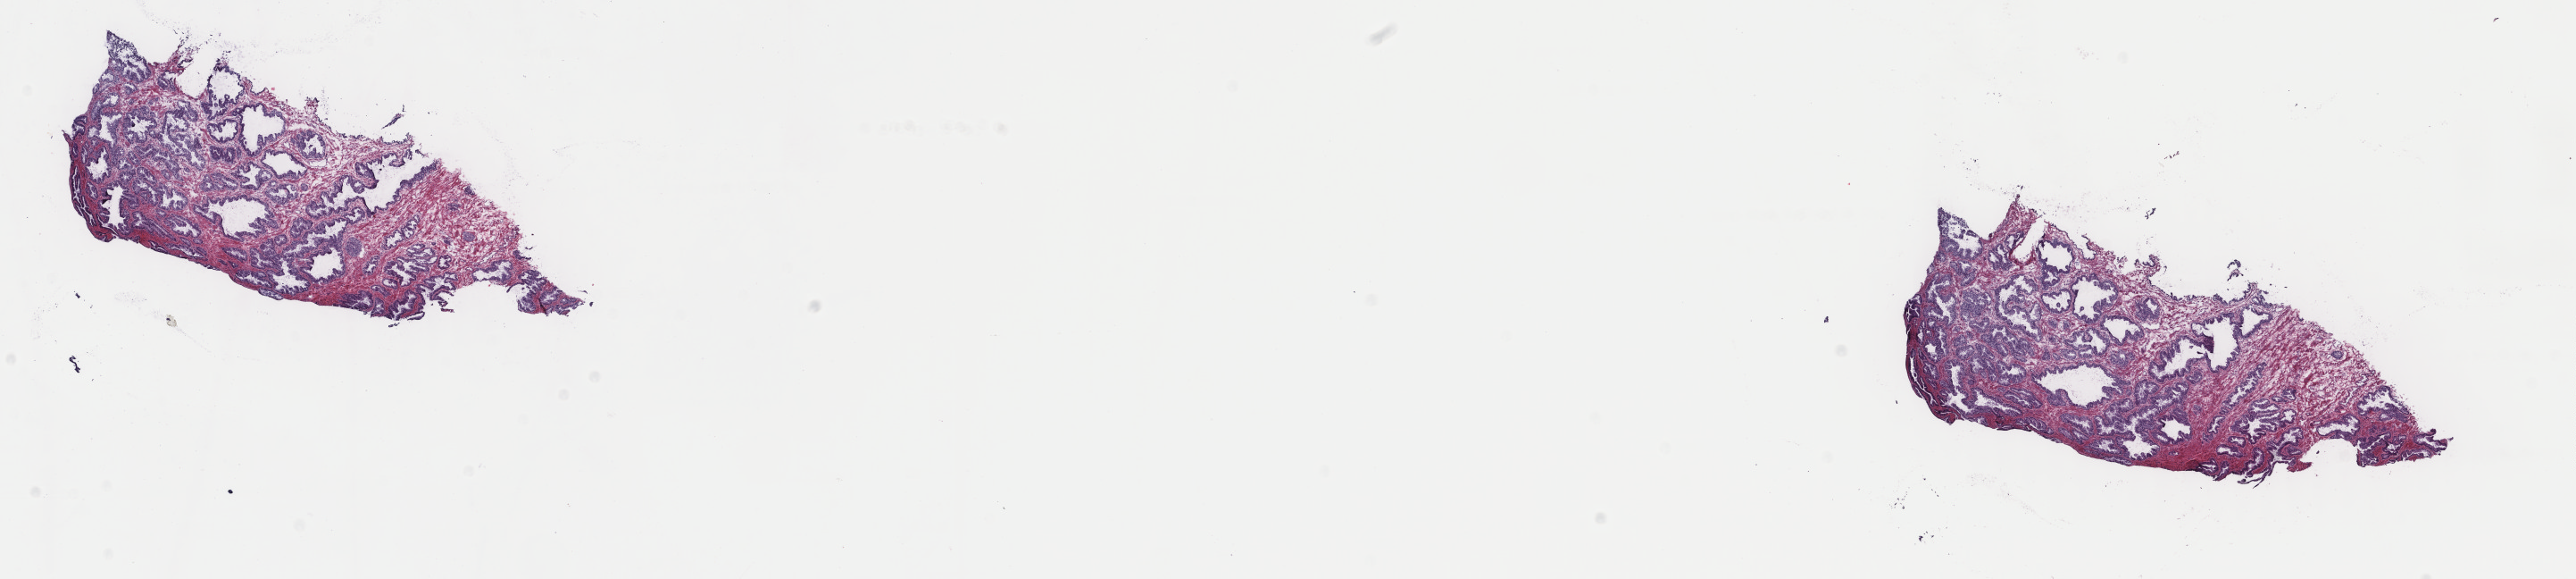
Hematoxylin and eosin (H&E) stained whole-slide image — shown as a low-resolution overview of the whole scanned area (about 22.9 x 5.1 mm); frozen section from the top of the tissue portion; sample: primary tumour, prostate. Male, age 66 years at initial diagnosis. Gleason score: 8 (4+4). Composition of this section per pathologist review: tumour cells 60%, tumour nuclei 100%, normal cells 0%, stromal cells 40%, necrosis 0%. Infiltration values recorded for this section: lymphocyte infiltration 1%, monocyte infiltration 0%, neutrophil infiltration 0%.
Lymph nodes positive (case pathology): 0 of 10 examined. Diagnosis: Adenocarcinoma, NOS. Laterality: bilateral.